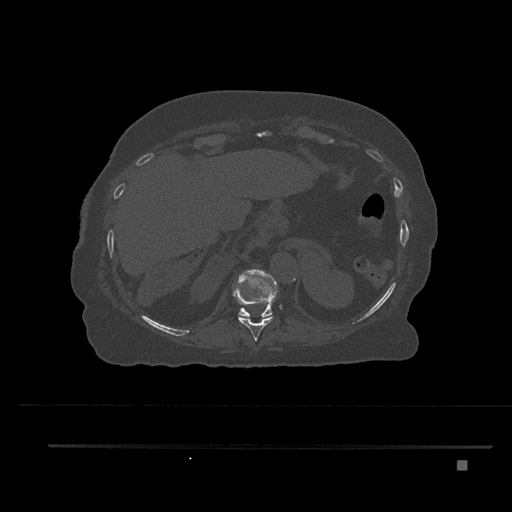
CT including the spine, one axial slice. Position 338 of 797 along the scan axis. Reconstruction kernel Br40s/3. 120 kVp. Bone window (W 1800 / L 400 HU). 512 × 512 image matrix. Patient: female, 76 years. Case-level facts recorded for this patient, not image findings: primary cancer: lung; vertebrae with lytic lesions (as recorded): T11, L3.
Structures marked on this image (semi-automatically segmented with operator editing):
- T10 vertebra: bounding box [x1, y1, x2, y2] px = [233, 285, 275, 341]
- T11 vertebra: [238, 269, 278, 317]